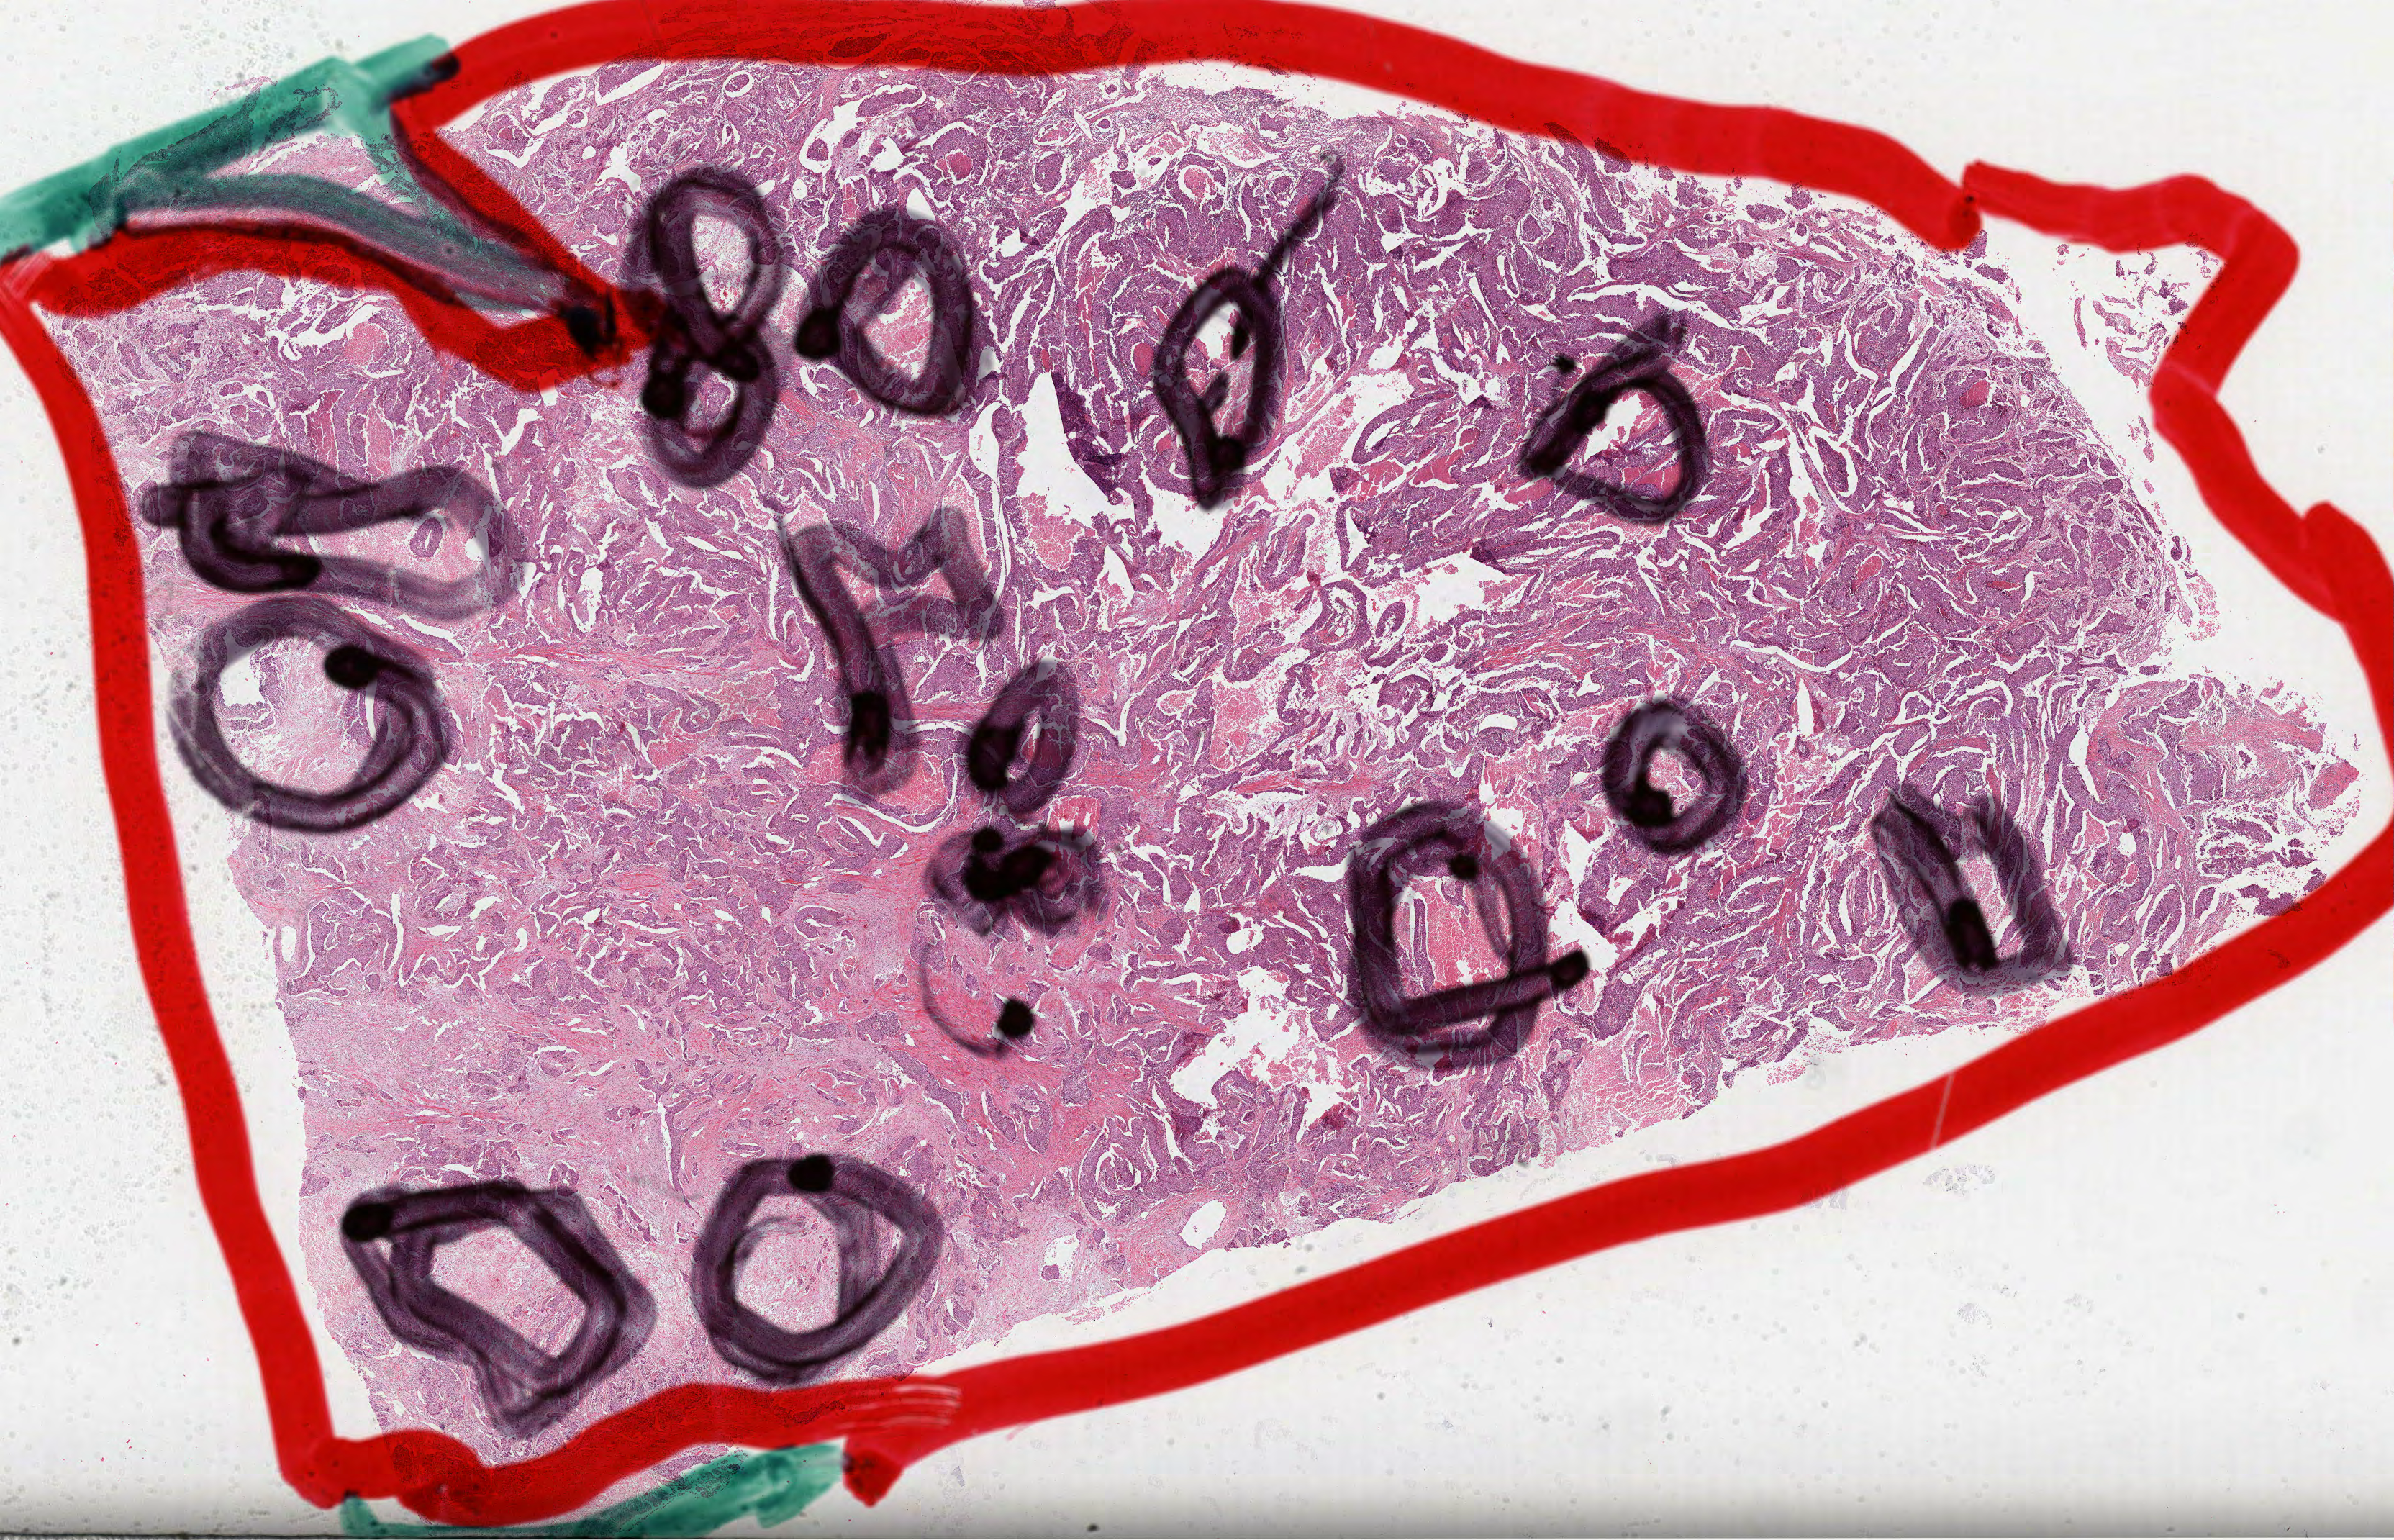
H&E-stained whole-slide image, whole scanned area (about 26.8 x 17.3 mm, slide scanned at 40x) shown as a low-resolution overview. Formalin-fixed paraffin-embedded (FFPE) diagnostic section. Lung, primary tumour sample. Patient: male, age at initial diagnosis 46 years.
TNM: T2a N0 M0. Laterality: left. Diagnosis: Squamous cell carcinoma, NOS. AJCC pathologic stage: IB.